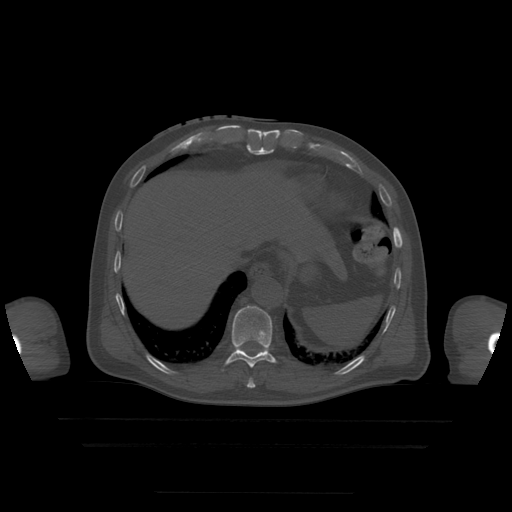
CT including the spine, one axial slice. Slice 241 of 522 in the series (ordered by position). Bone window (W 1800 / L 400 HU). 1.25 mm slice thickness. 512 × 512 image matrix. Patient age 68 years. Case-level facts recorded for this patient, not image findings: primary cancer: urothelial.
Outlined on this slice (semi-automatic segmentation, software-assisted and operator-edited):
- T10 vertebra: bounding box [x1, y1, x2, y2] px = [226, 306, 276, 368]
- T9 vertebra: [247, 379, 255, 389]